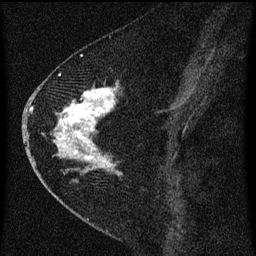
Breast MRI (dynamic contrast-enhanced), one sagittal slice; position 29 of 60 along the scan axis; dynamic contrast-enhanced series, image 2 of 3 at this slice position (ordered by acquisition); 1.5 T; TE 4.2 ms, TR 8 ms; 2 mm slice thickness; 256 × 256 image matrix, field of view 180 × 180 mm. Female patient, age 47 years.
Outlined on this slice (semi-automatically segmented with operator editing):
- analysis volume of interest (the breast-tissue region the enhancement analysis was run in; not a lesion): bounding box [x1, y1, x2, y2] px = [38, 76, 127, 193]
- tumour enhancement mask (voxels above the 70 % enhancement threshold inside the analysis volume of interest): [53, 76, 120, 175]